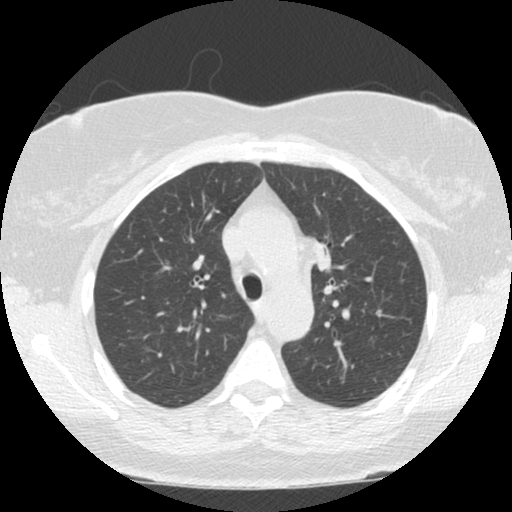
Axial slice from a low-dose chest CT screening exam, second screening round (one year after baseline), lung window (W 1500 / L -600 HU), 2.5 mm slice thickness, standard (soft-tissue) reconstruction kernel (STANDARD). Female participant, aged 66 years at enrolment. Former smoker at enrolment.
Expert reader's lesion annotation, bounding box (x1, y1, x2, y2) in pixels: (292, 233, 344, 286). The exam's reader record, not a measurement of the box and not confirmed to be the same lesion: non-calcified nodule or mass ≥4 mm, left upper lobe, 12 × 9 mm, smooth margins, soft tissue attenuation, pre-existing on the prior screen: no. Official screen result: positive, other. Participant outcome: lung cancer diagnosed 196 days after this screen — small cell carcinoma, NOS, left upper lobe, stage IIIA (AJCC 6th edition), 50 mm at pathology.